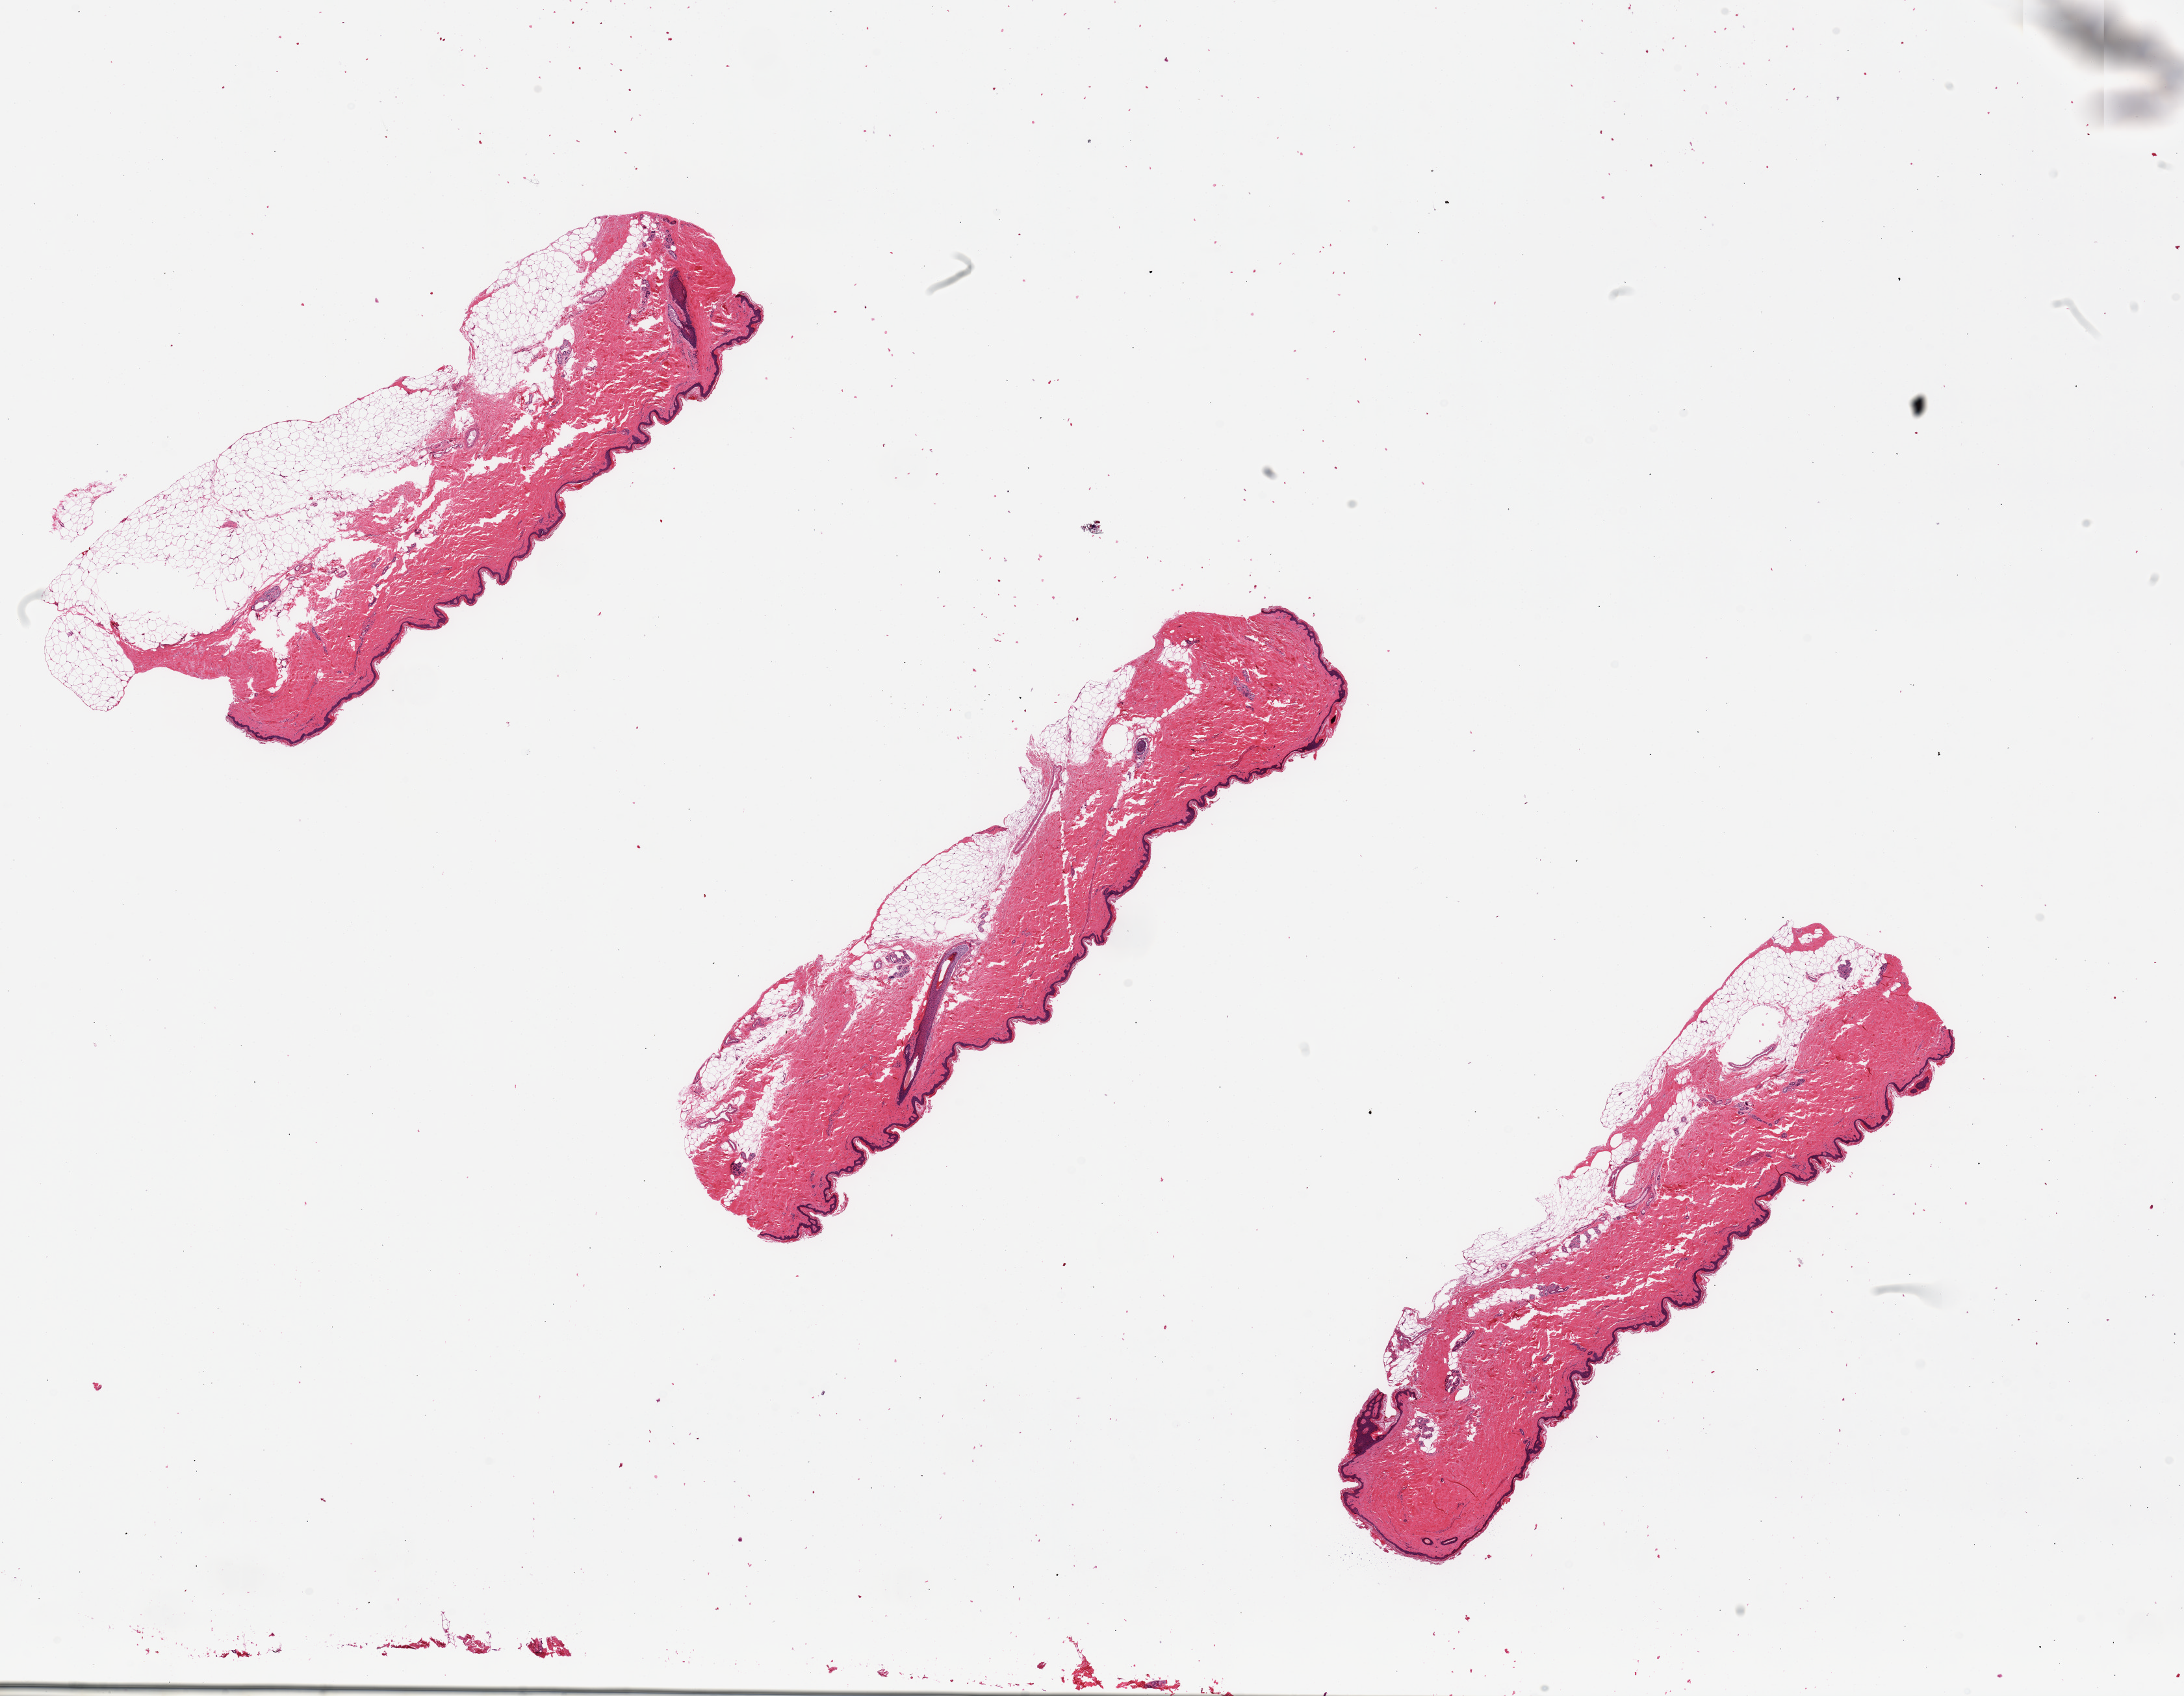
Digitized hematoxylin and eosin (H&E)-stained section — whole scanned area (about 26.6 x 20.6 mm) shown as a low-resolution overview; PAXgene-fixed paraffin-embedded (PFPE) section; target tissue: skin of lower leg; tissue donor sample.
Review note (as recorded): 3 pieces.